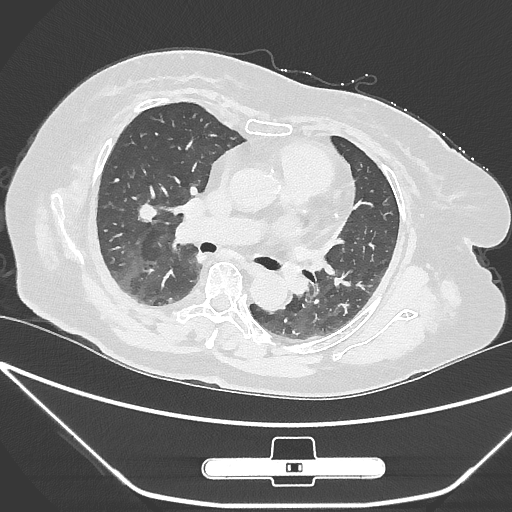
Chest CT, one axial slice; position 154 of 245 along the scan axis; reconstruction kernel IMR1,SharpPlus; lung window (W 1500 / L -600 HU); 1 mm slice thickness; 512 × 512 image matrix, field of view 365 × 365 mm. Female patient, age 65 years. From the clinical record (not read from this slice): clinical TNM (as recorded): T1c N0 M0; histopathological grade: G3.
Structures marked on this image (rectangle marked by the reading radiologist):
- lung tumour (recorded histology: adenocarcinoma): bounding box (x1, y1, x2, y2) in pixels: (139, 200, 160, 226)